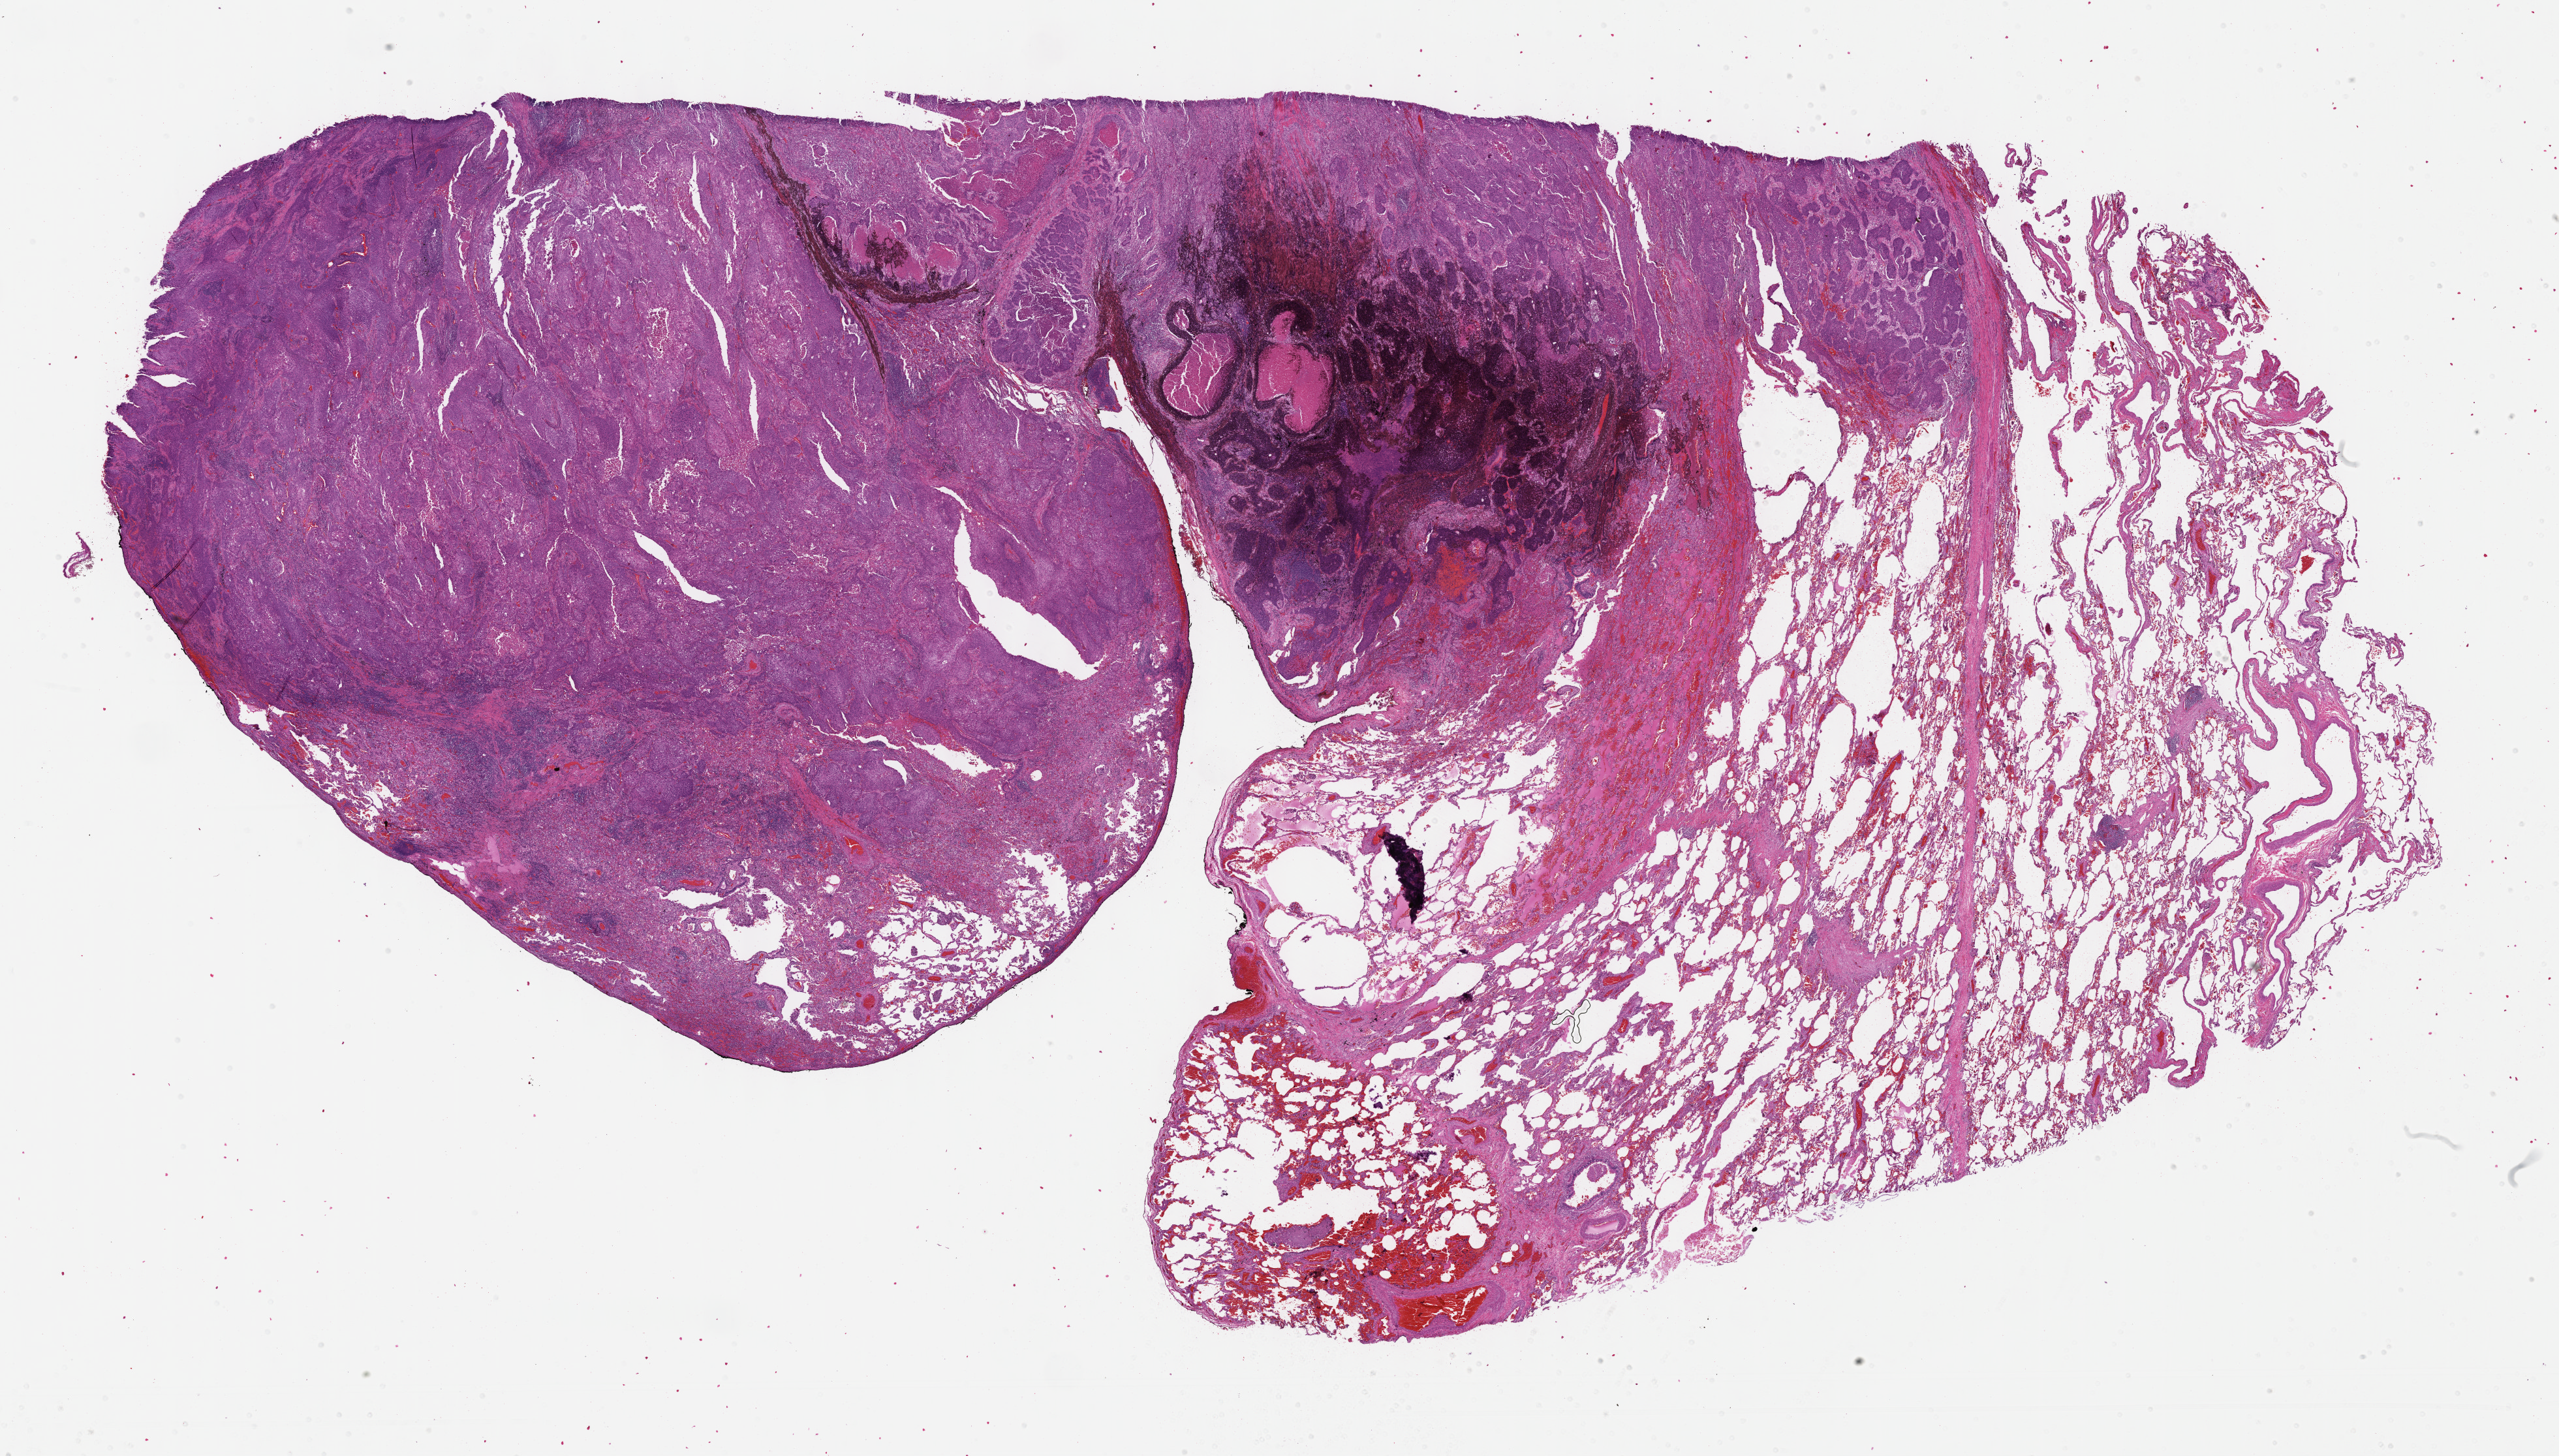
H&E whole-slide image, shown as a low-resolution overview of the whole scanned area (about 31.7 x 18.0 mm, acquisition: 40x scan), formalin-fixed paraffin-embedded (FFPE) diagnostic section, lung, primary tumour sample. Patient: male, age at initial diagnosis 60 years.
Diagnosis: Squamous cell carcinoma, NOS (upper lobe, lung). AJCC pathologic stage: IB. Laterality: right. TNM: T2a N0 MX.